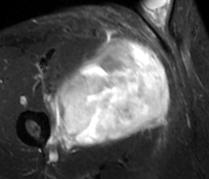
MRI of an extremity soft-tissue mass, one axial slice. Slice 49 of 89 in the series (ordered by position). STIR. MR volume resampled by the dataset authors to the PET/CT grid (not the native acquisition matrix). 3.27 mm slice thickness. 209 × 179 image matrix, field of view 204 × 175 mm. Male patient. From the clinical record (not read from this slice): histological type: undifferentiated - pleiomorphic; grade: high; site of the primary tumour: right thigh.
Outlined on this slice (expert contour drawn on MRI and transferred to this co-registered scan by the dataset authors):
- gross tumour volume including surrounding oedema: box from (x=46, y=37) to (x=170, y=150) px
- gross tumour volume (mass): (x=55, y=39)–(x=170, y=147)